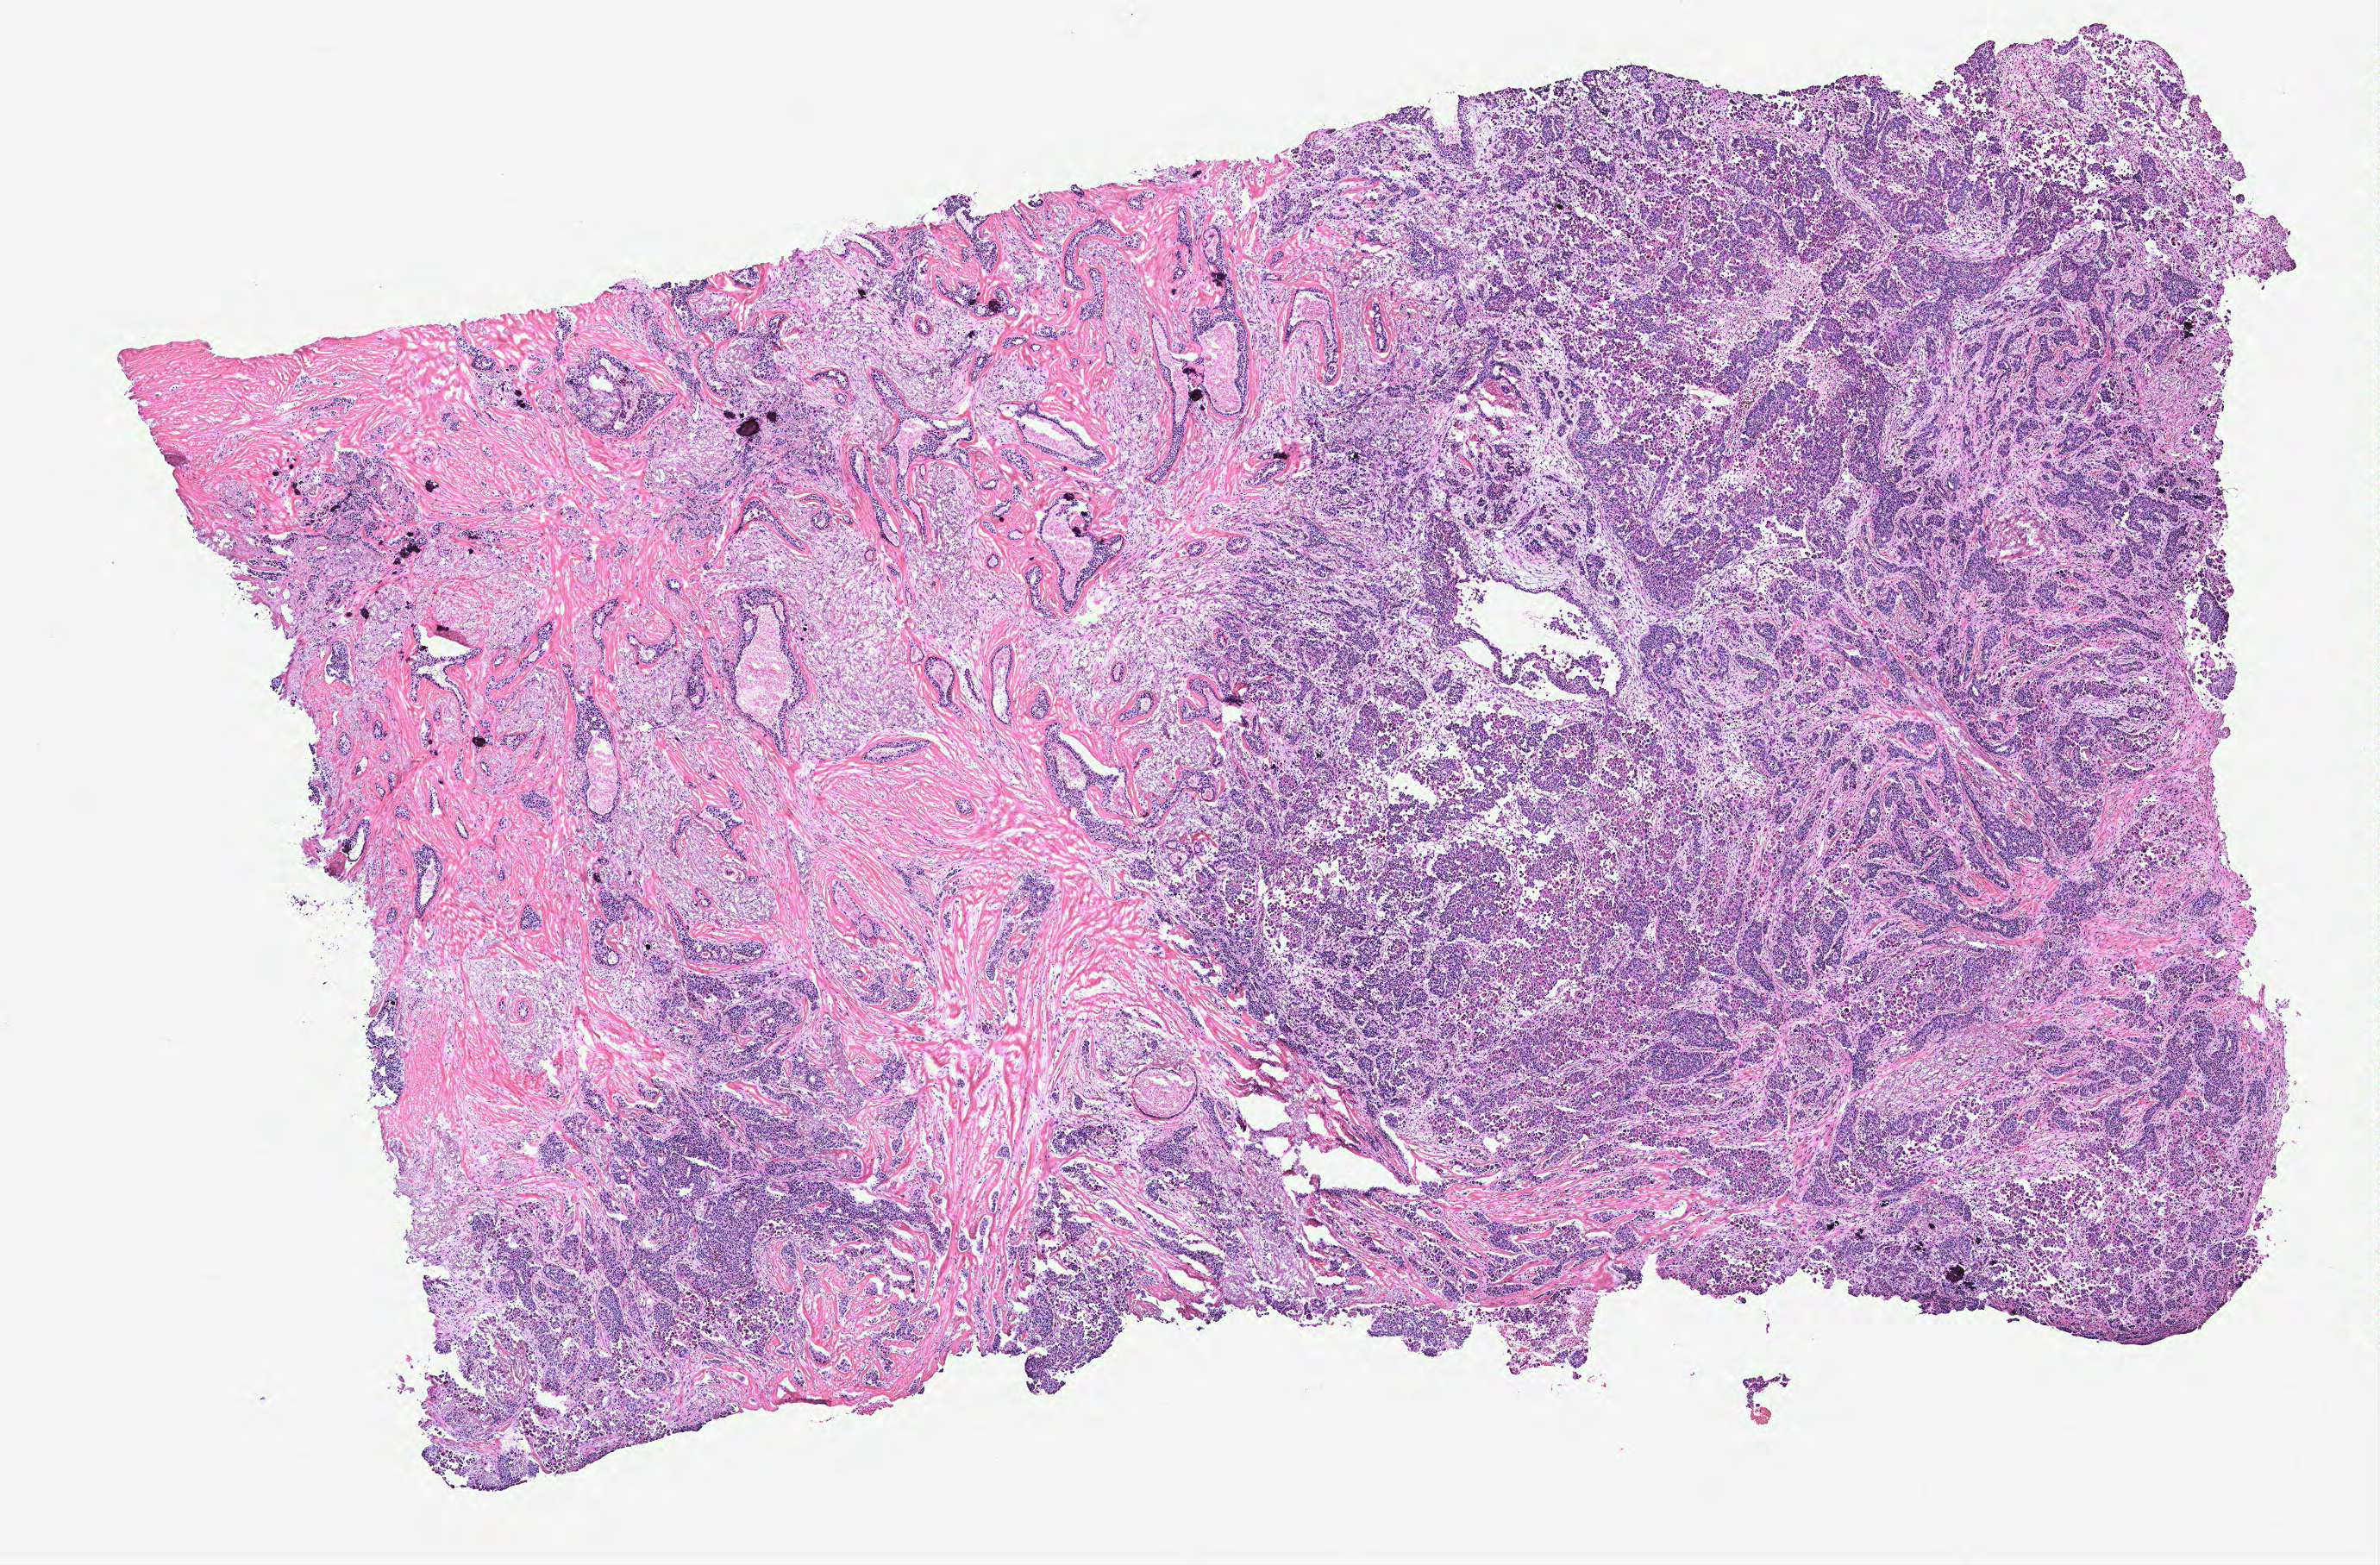
Whole-slide histology image, H&E-stained, whole scanned area (about 11.0 x 7.3 mm, acquisition: 40x scan) shown as a low-resolution overview. Tumour tissue sample, breast. Female, 59 y/o.
Histologic diagnosis: Infiltrating duct carcinoma, NOS. AJCC pathologic stage: IIA.